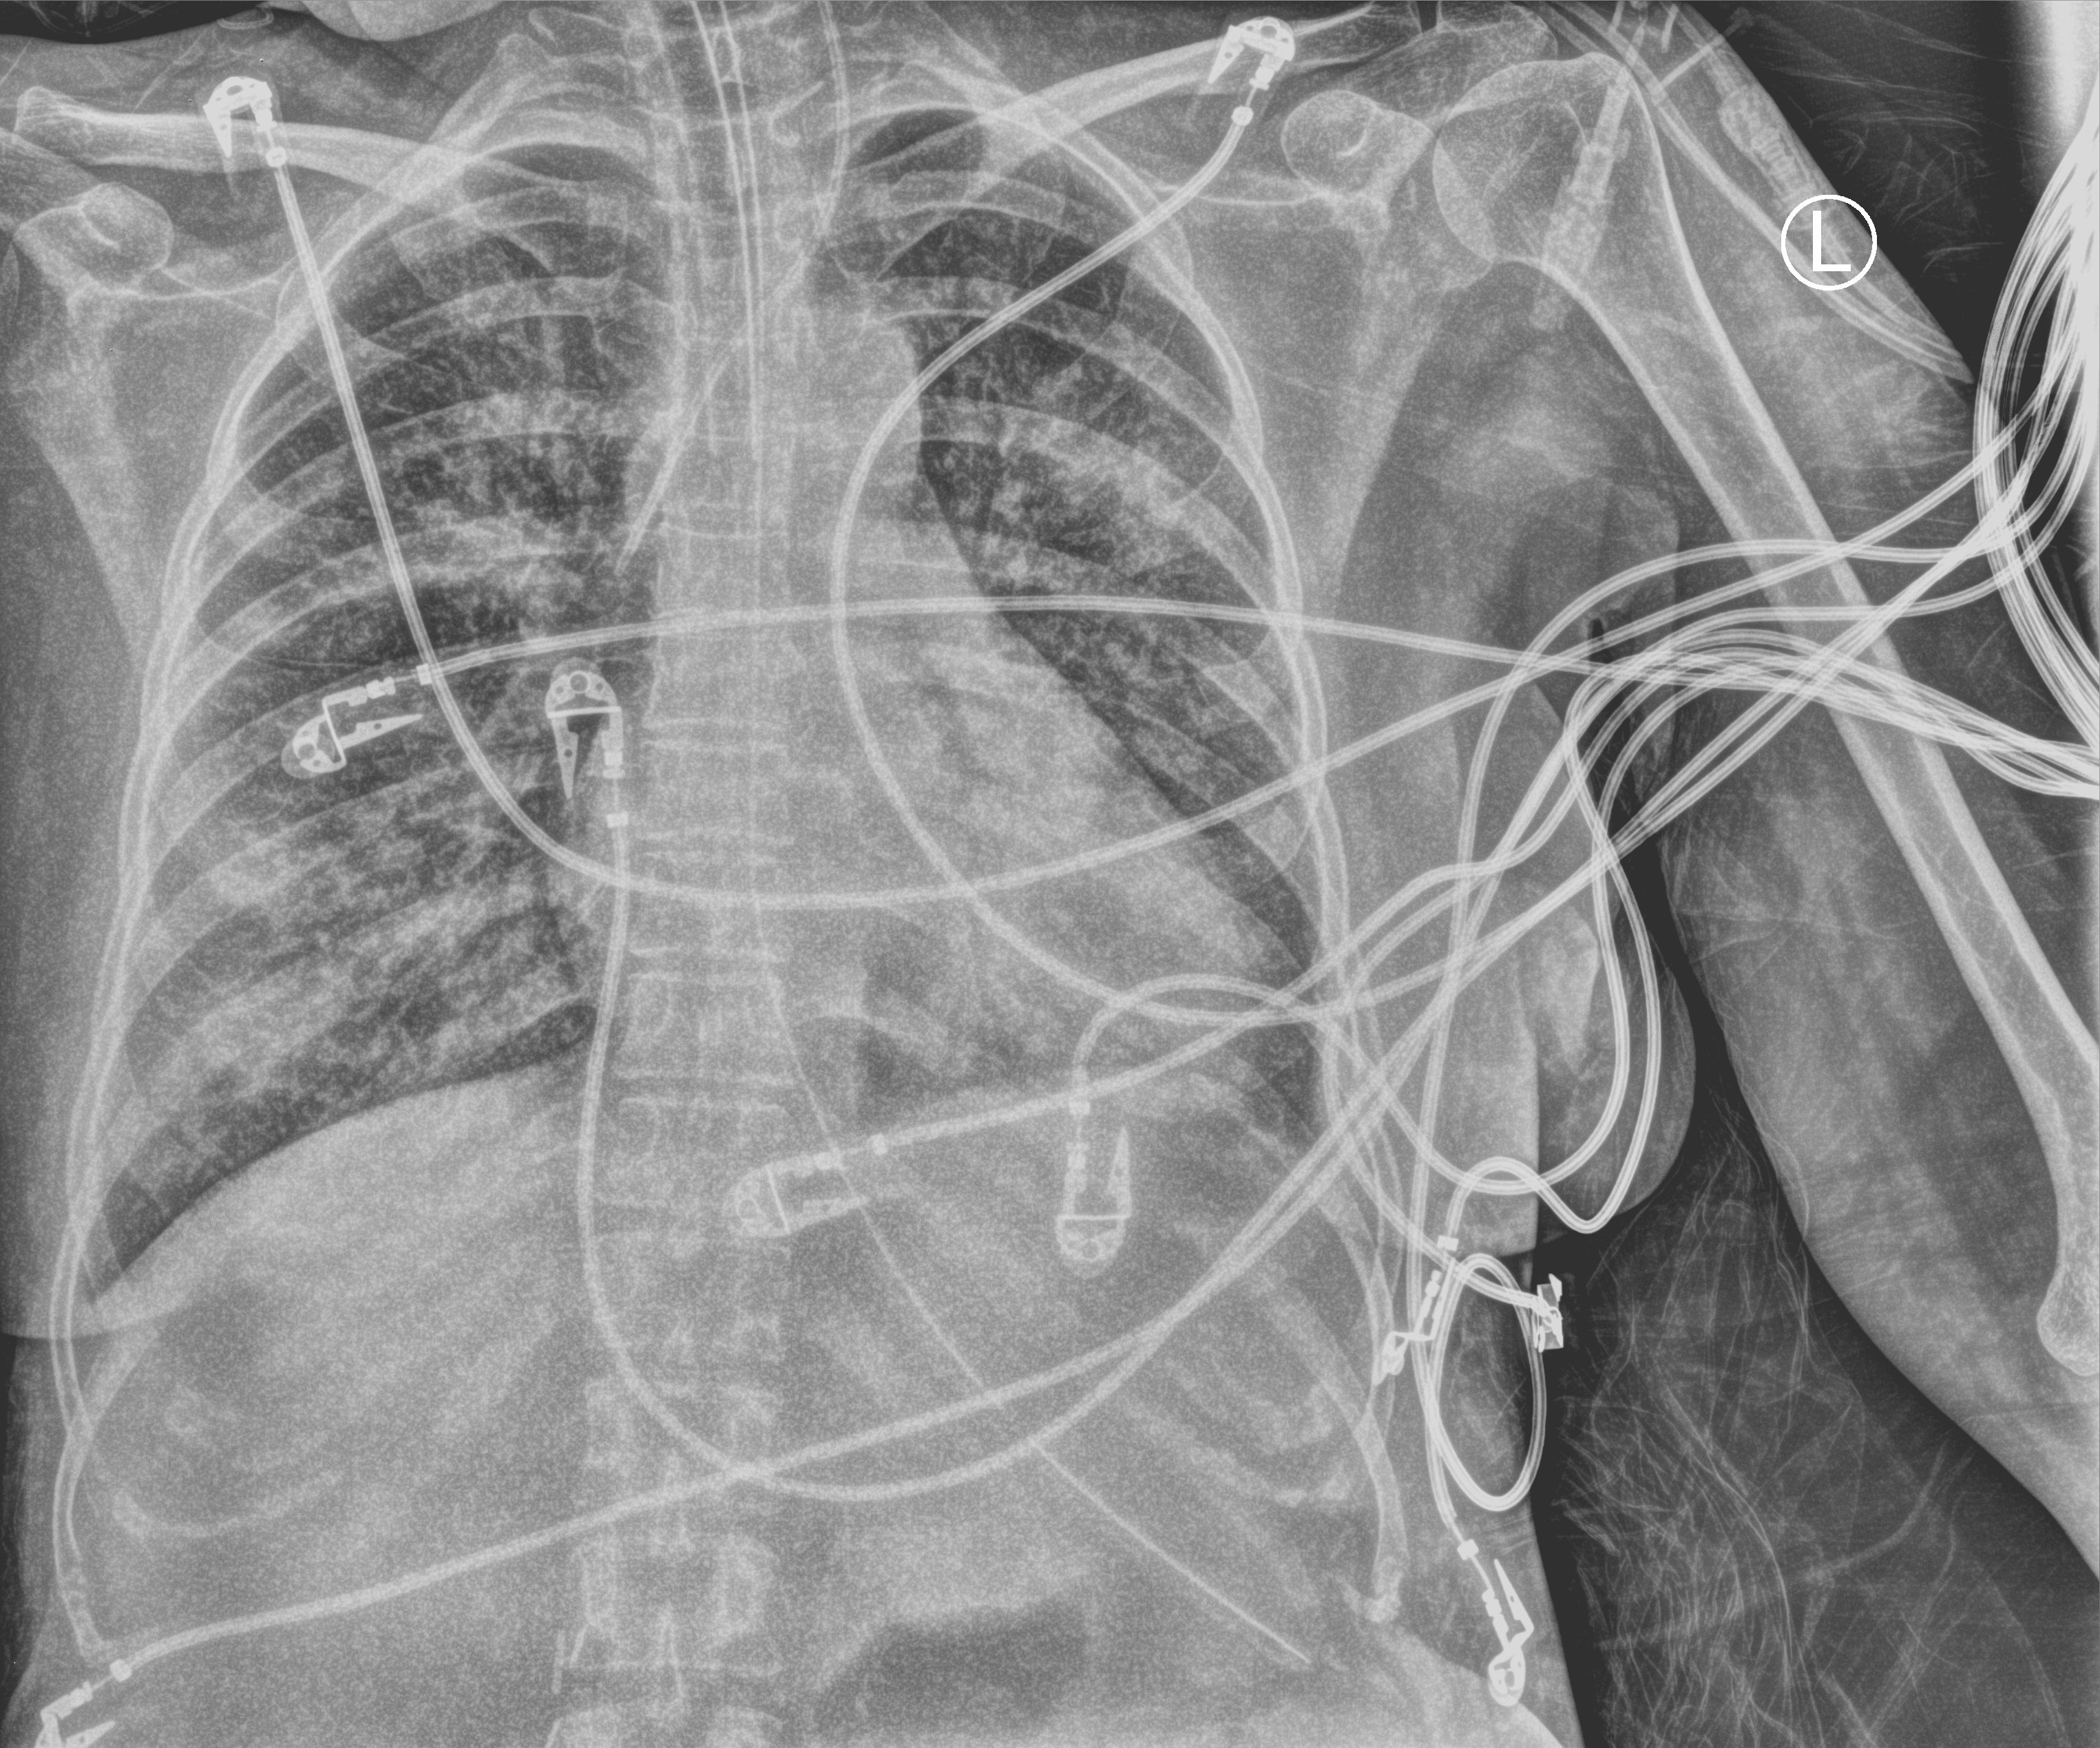
Portable chest radiograph; anteroposterior (AP) projection. Patient hospitalised with COVID-19, aged 18–59 years.
Hospital-stay facts (about this admission, not read from this image; timing relative to this image not recorded): mechanically ventilated during this hospital stay: yes.